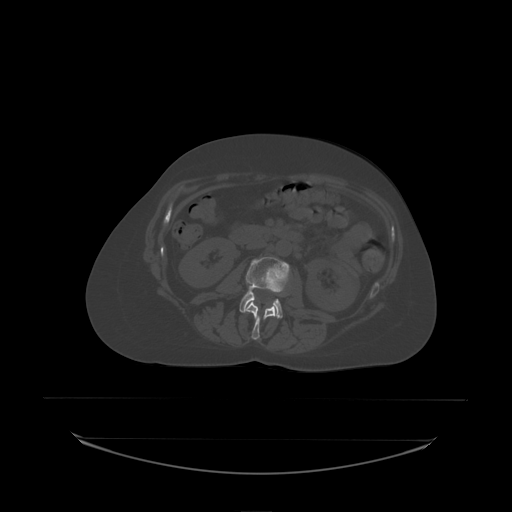
CT including the spine, one axial slice; slice 66 of 242 in the series (ordered by position); bone window (W 1800 / L 400 HU); 512 × 512 image matrix, field of view 500 × 500 mm. Patient: female, 53 years. Case-level facts recorded for this patient, not image findings: primary cancer: lung; vertebrae with lytic lesions (as recorded): T7, L1.
Outlined on this slice (semi-automatic segmentation, software-assisted and operator-edited):
- L2 vertebra: box from (x=246, y=302) to (x=277, y=338) px
- L3 vertebra: (x=240, y=257)–(x=290, y=319)